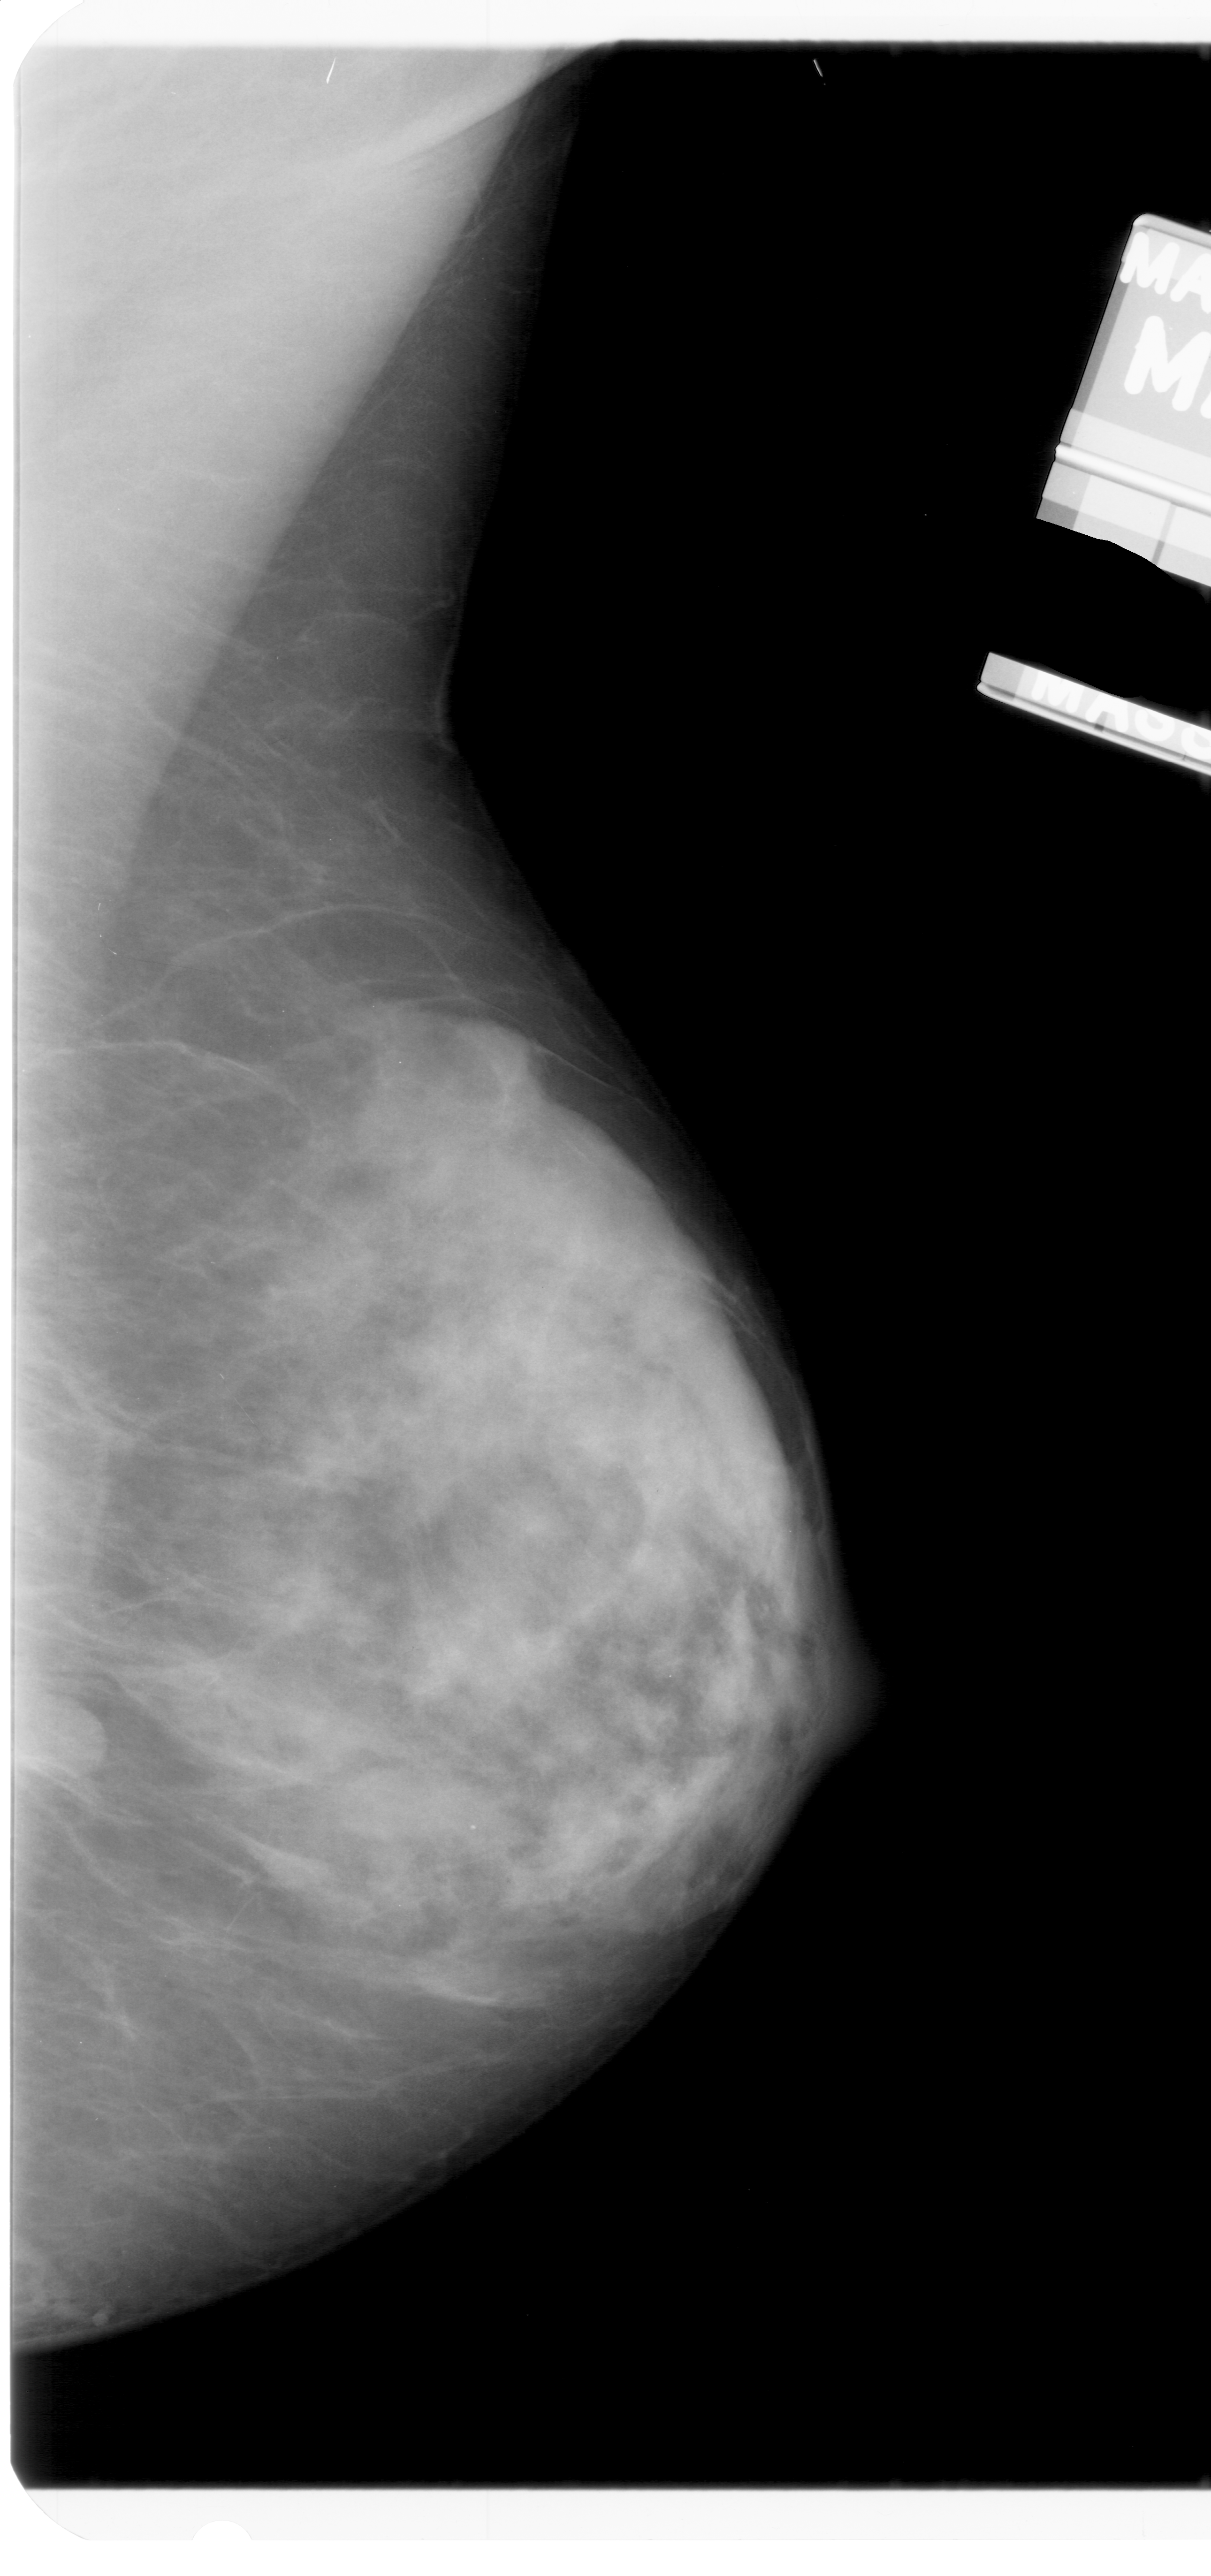
Digitized screen-film mammogram; right breast; mediolateral oblique (MLO) view; BI-RADS breast density category 4 (scale 1–4); 1211 × 2576 image matrix.
Marked abnormalities (boxes around the expert regions of interest):
- mass, shape oval, margins obscured; BI-RADS assessment category 3; subtlety rating 3 on a 1 (subtle) to 5 (obvious) scale; pathology (as recorded): benign: bounding box [x1, y1, x2, y2] px = [0, 1675, 110, 1800]